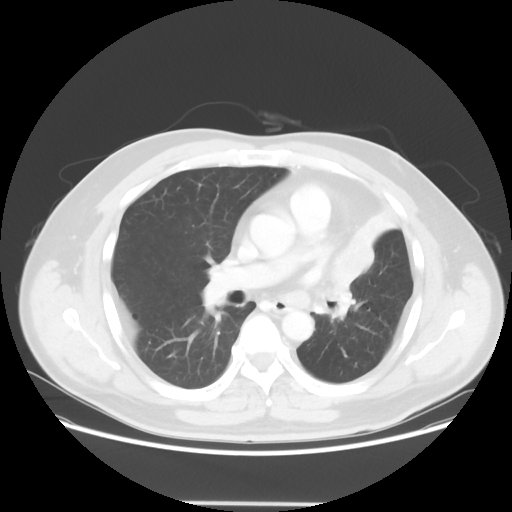
Chest CT, one axial slice. Position 35 of 62 along the scan axis. 120 kVp. Lung window (W 1500 / L -600 HU). 5 mm slice thickness. 512 × 512 image matrix. Male patient, age 49 years. Case-level facts recorded for this patient, not image findings: clinical TNM (as recorded): T3 N3 M1c.
Outlined on this slice (bounding box drawn by a radiologist):
- lung tumour (recorded histology: squamous cell carcinoma): bounding box <323,233,387,309> (left, top, right, bottom; pixels)